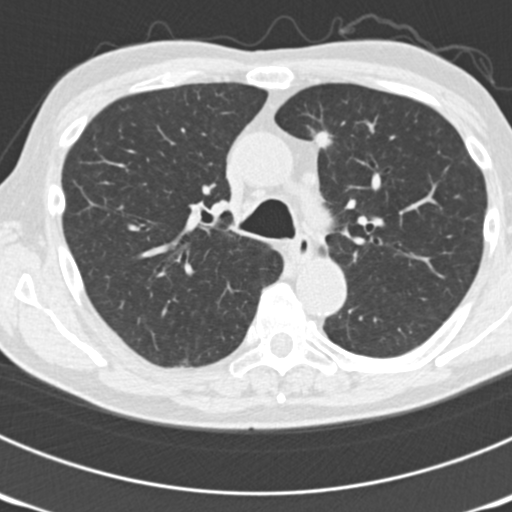
Low-dose screening chest CT, one axial slice; 120 kVp; lung window (W 1500 / L -600 HU); 2 mm slice thickness; 512 × 512 image matrix, field of view 300 × 300 mm.
Outlined on this slice (outlined manually by an expert reader):
- lesion 4 (tumor): bounding box <315,131,333,151> (left, top, right, bottom; pixels)